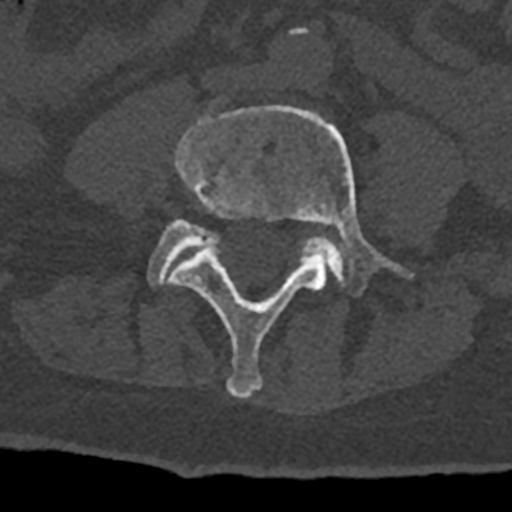
CT including the spine, one axial slice; slice 244 of 797 in the series (ordered by position); reconstruction kernel Br40s/3; bone window (W 1800 / L 400 HU); 512 × 512 image matrix, field of view 160 × 160 mm. Male patient, age 74 years. From the clinical record (not read from this slice): primary cancer: renal.
Outlined on this slice (semi-automatically segmented with operator editing):
- L4 vertebra: bounding box <167,106,414,399> (left, top, right, bottom; pixels)
- L5 vertebra: <147,219,344,285>